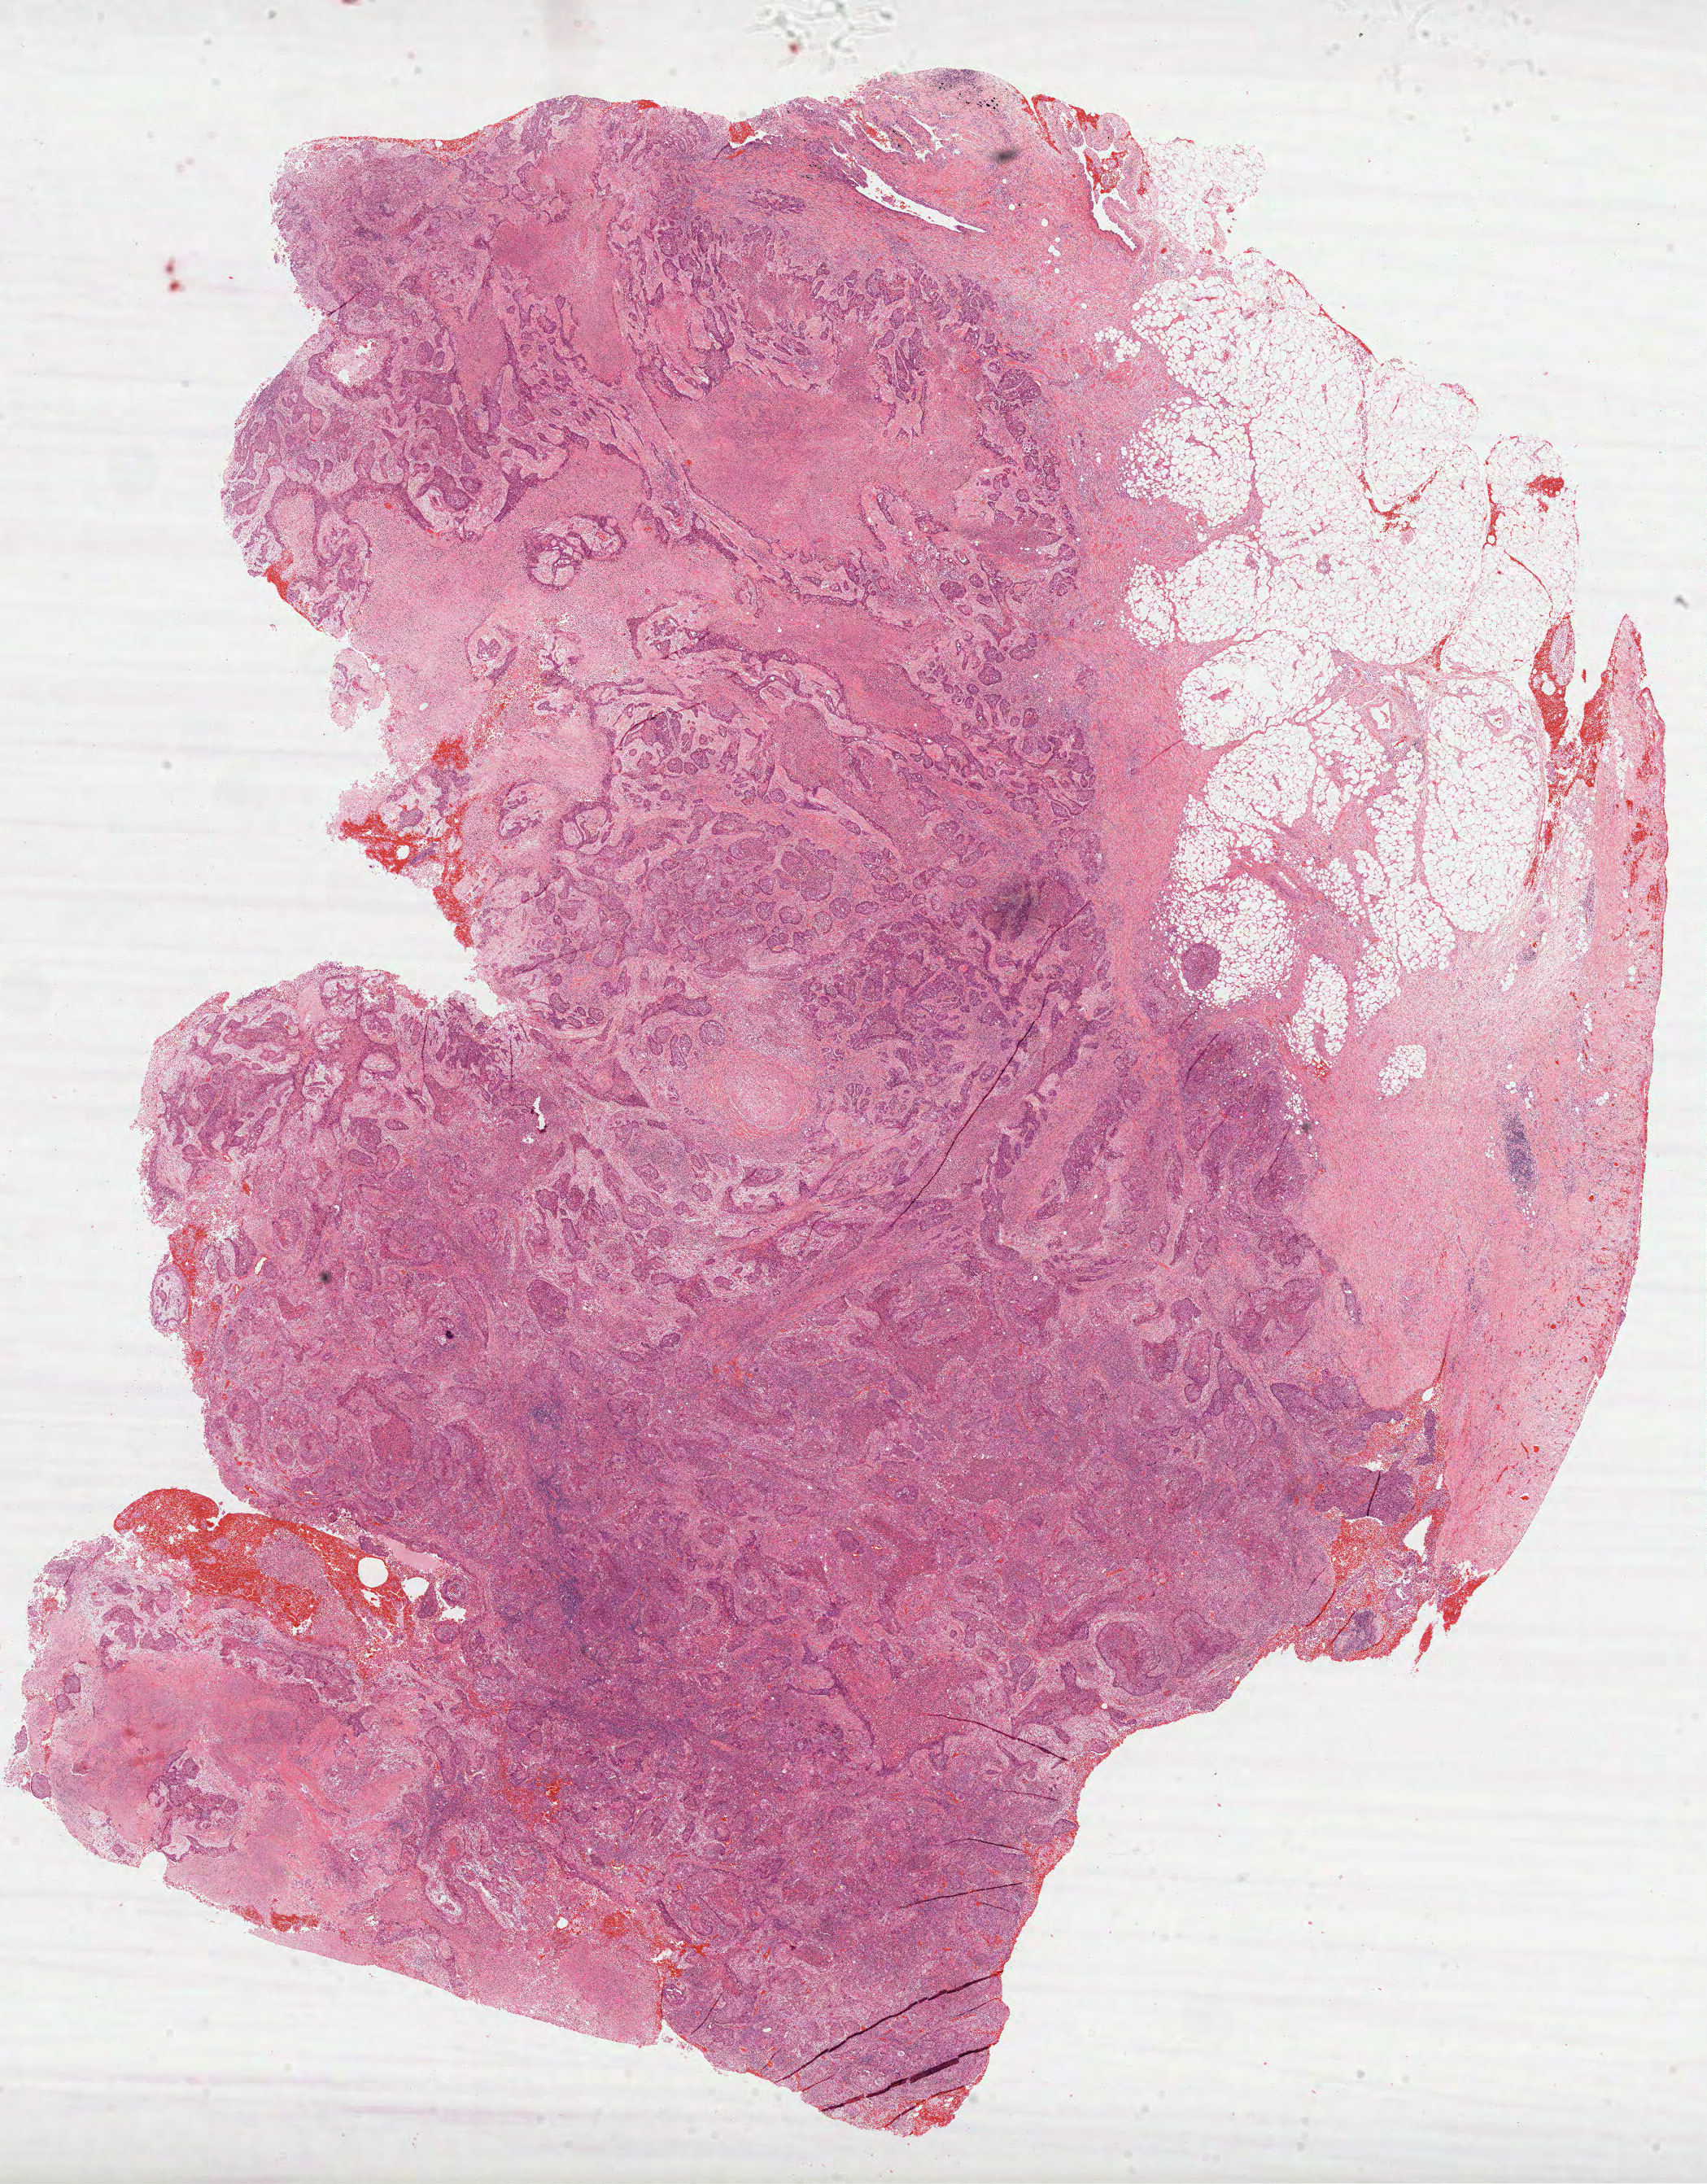
Whole-slide histology image, Hematoxylin and eosin (H&E) stained, whole scanned area (about 16.9 x 21.6 mm) shown as a low-resolution overview, formalin-fixed paraffin-embedded (FFPE) diagnostic section, sample: primary tumour, lung. Patient: male, age at initial diagnosis 65 years.
- histologic diagnosis: Squamous cell carcinoma, NOS (upper lobe, lung)
- laterality: left
- AJCC pathologic stage: IB (7th edition)